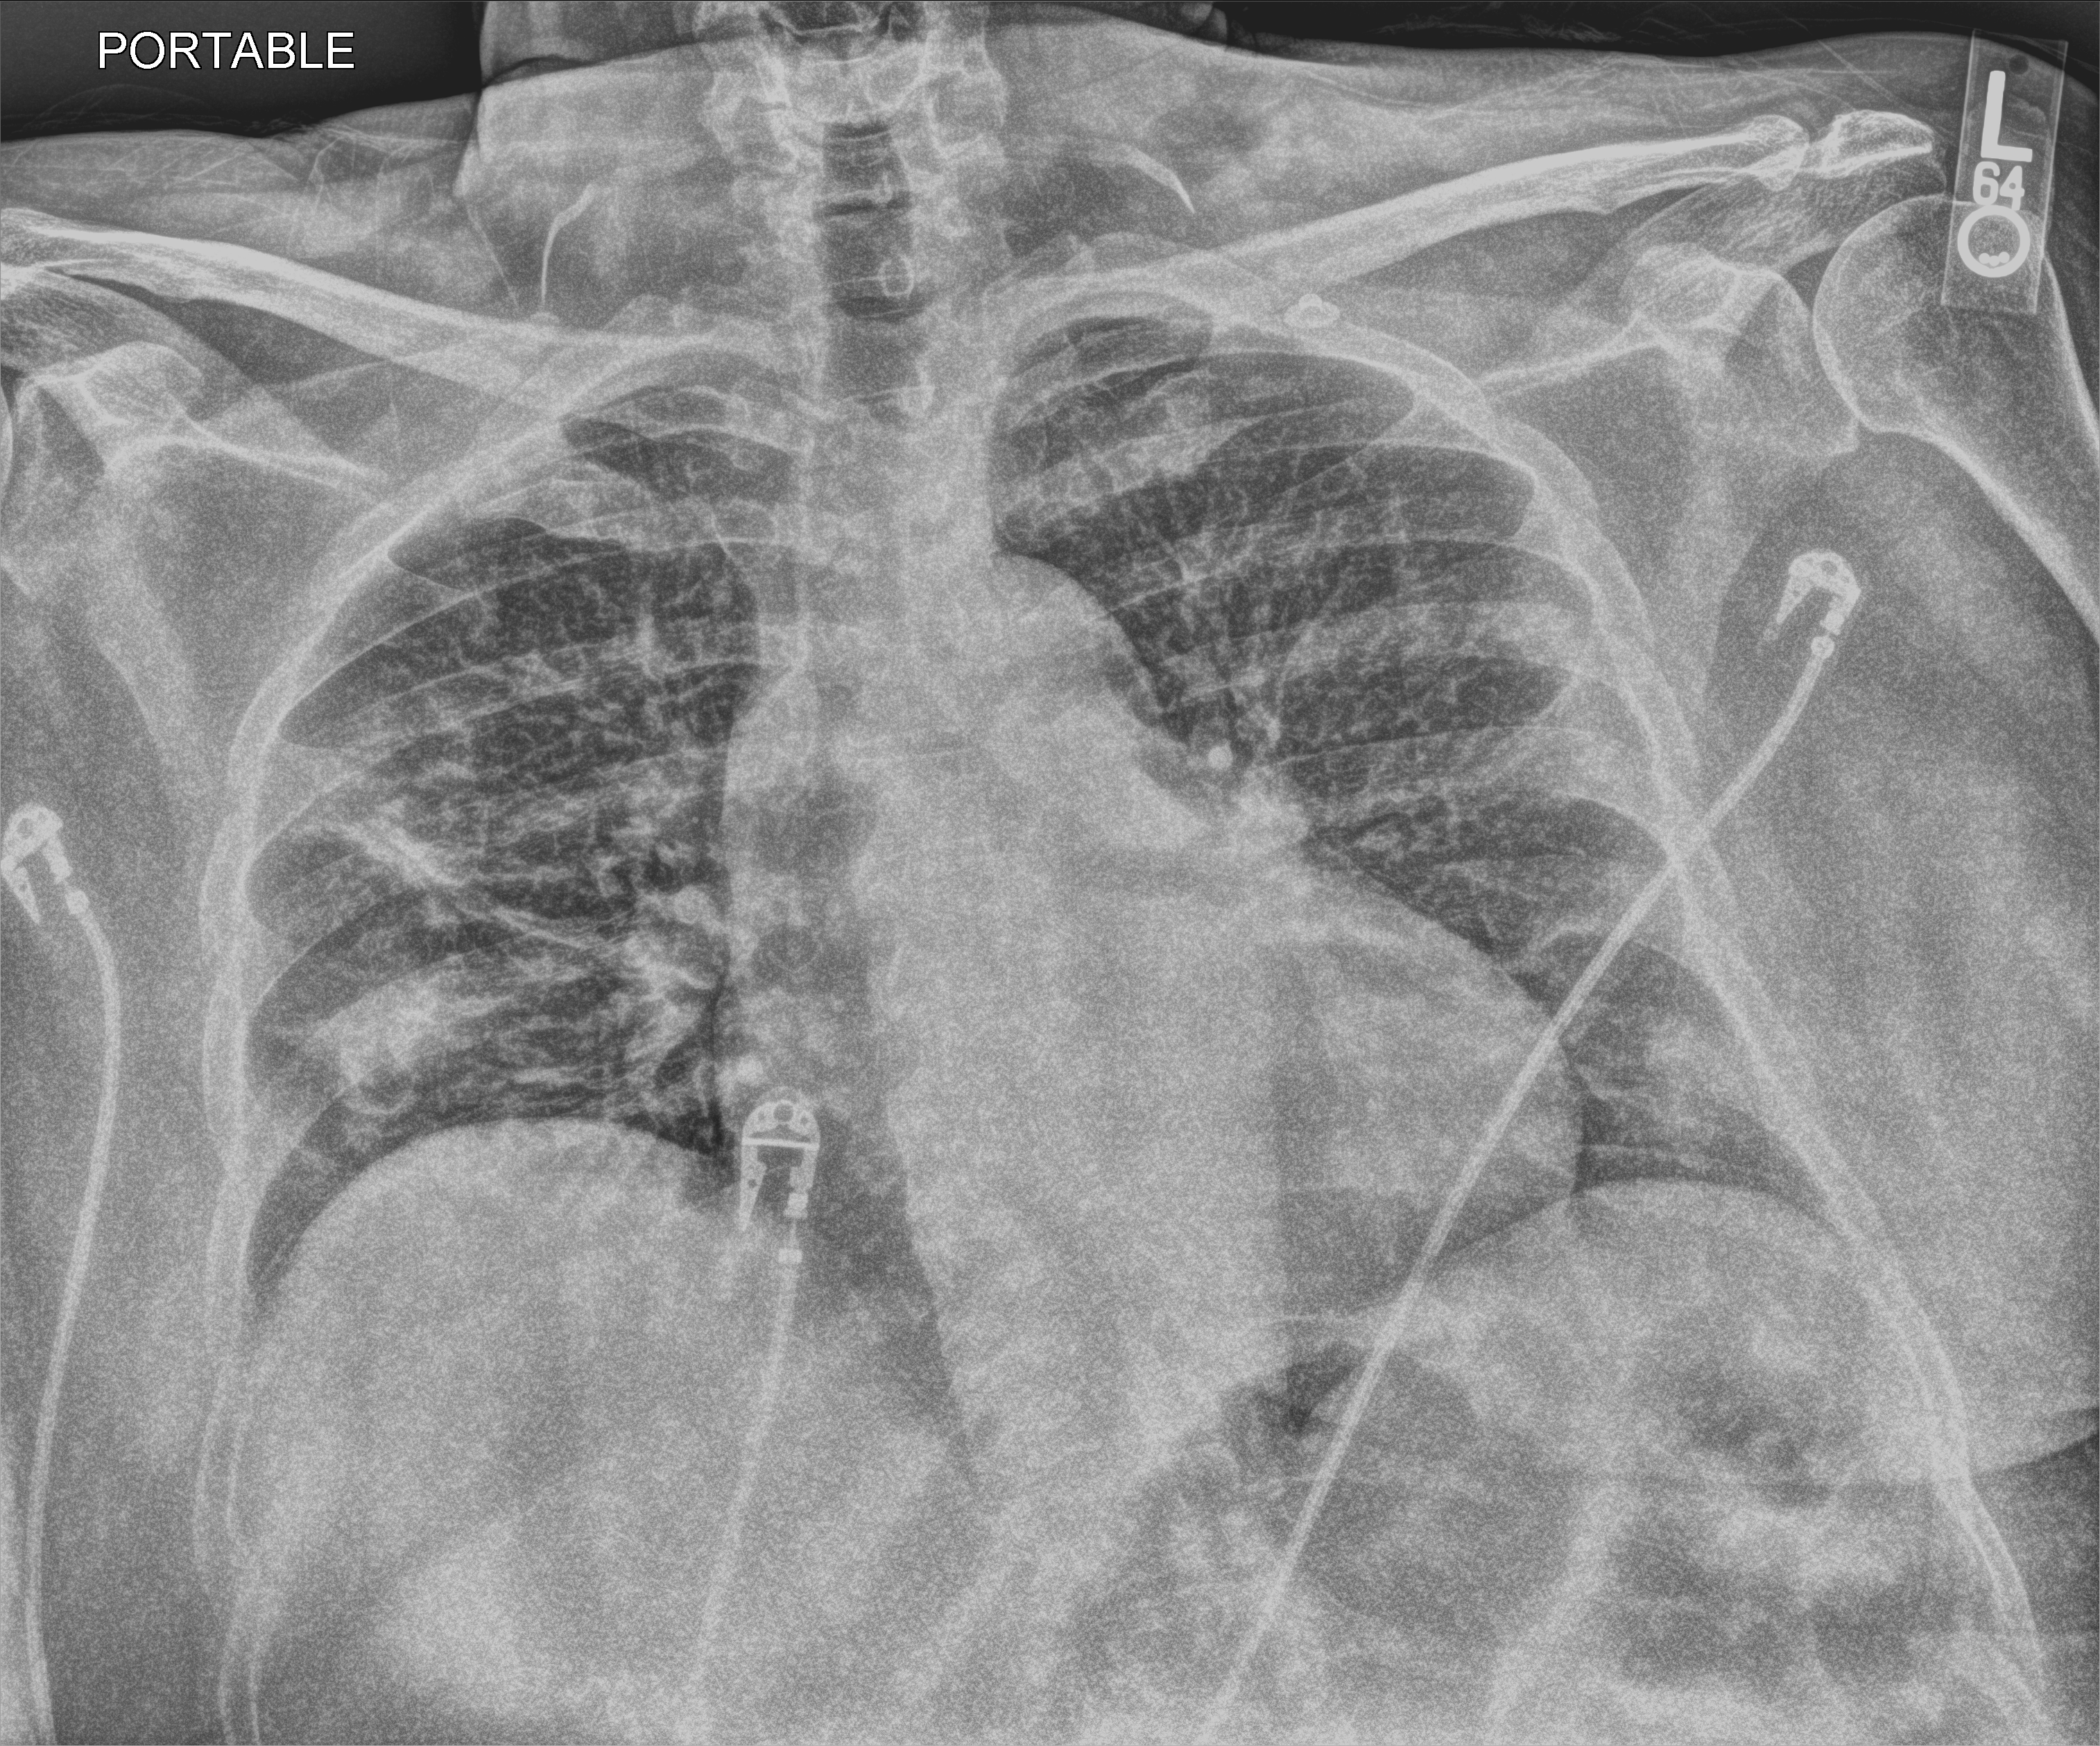
Portable chest radiograph; anteroposterior (AP) projection. Patient hospitalised with COVID-19; female, aged 60–74 years.
From the hospital-stay record, not from the radiograph (when in the stay this image was taken is not recorded): admitted to intensive care during this hospital stay: no; mechanically ventilated during this hospital stay: no; length of hospital stay: 7 days.